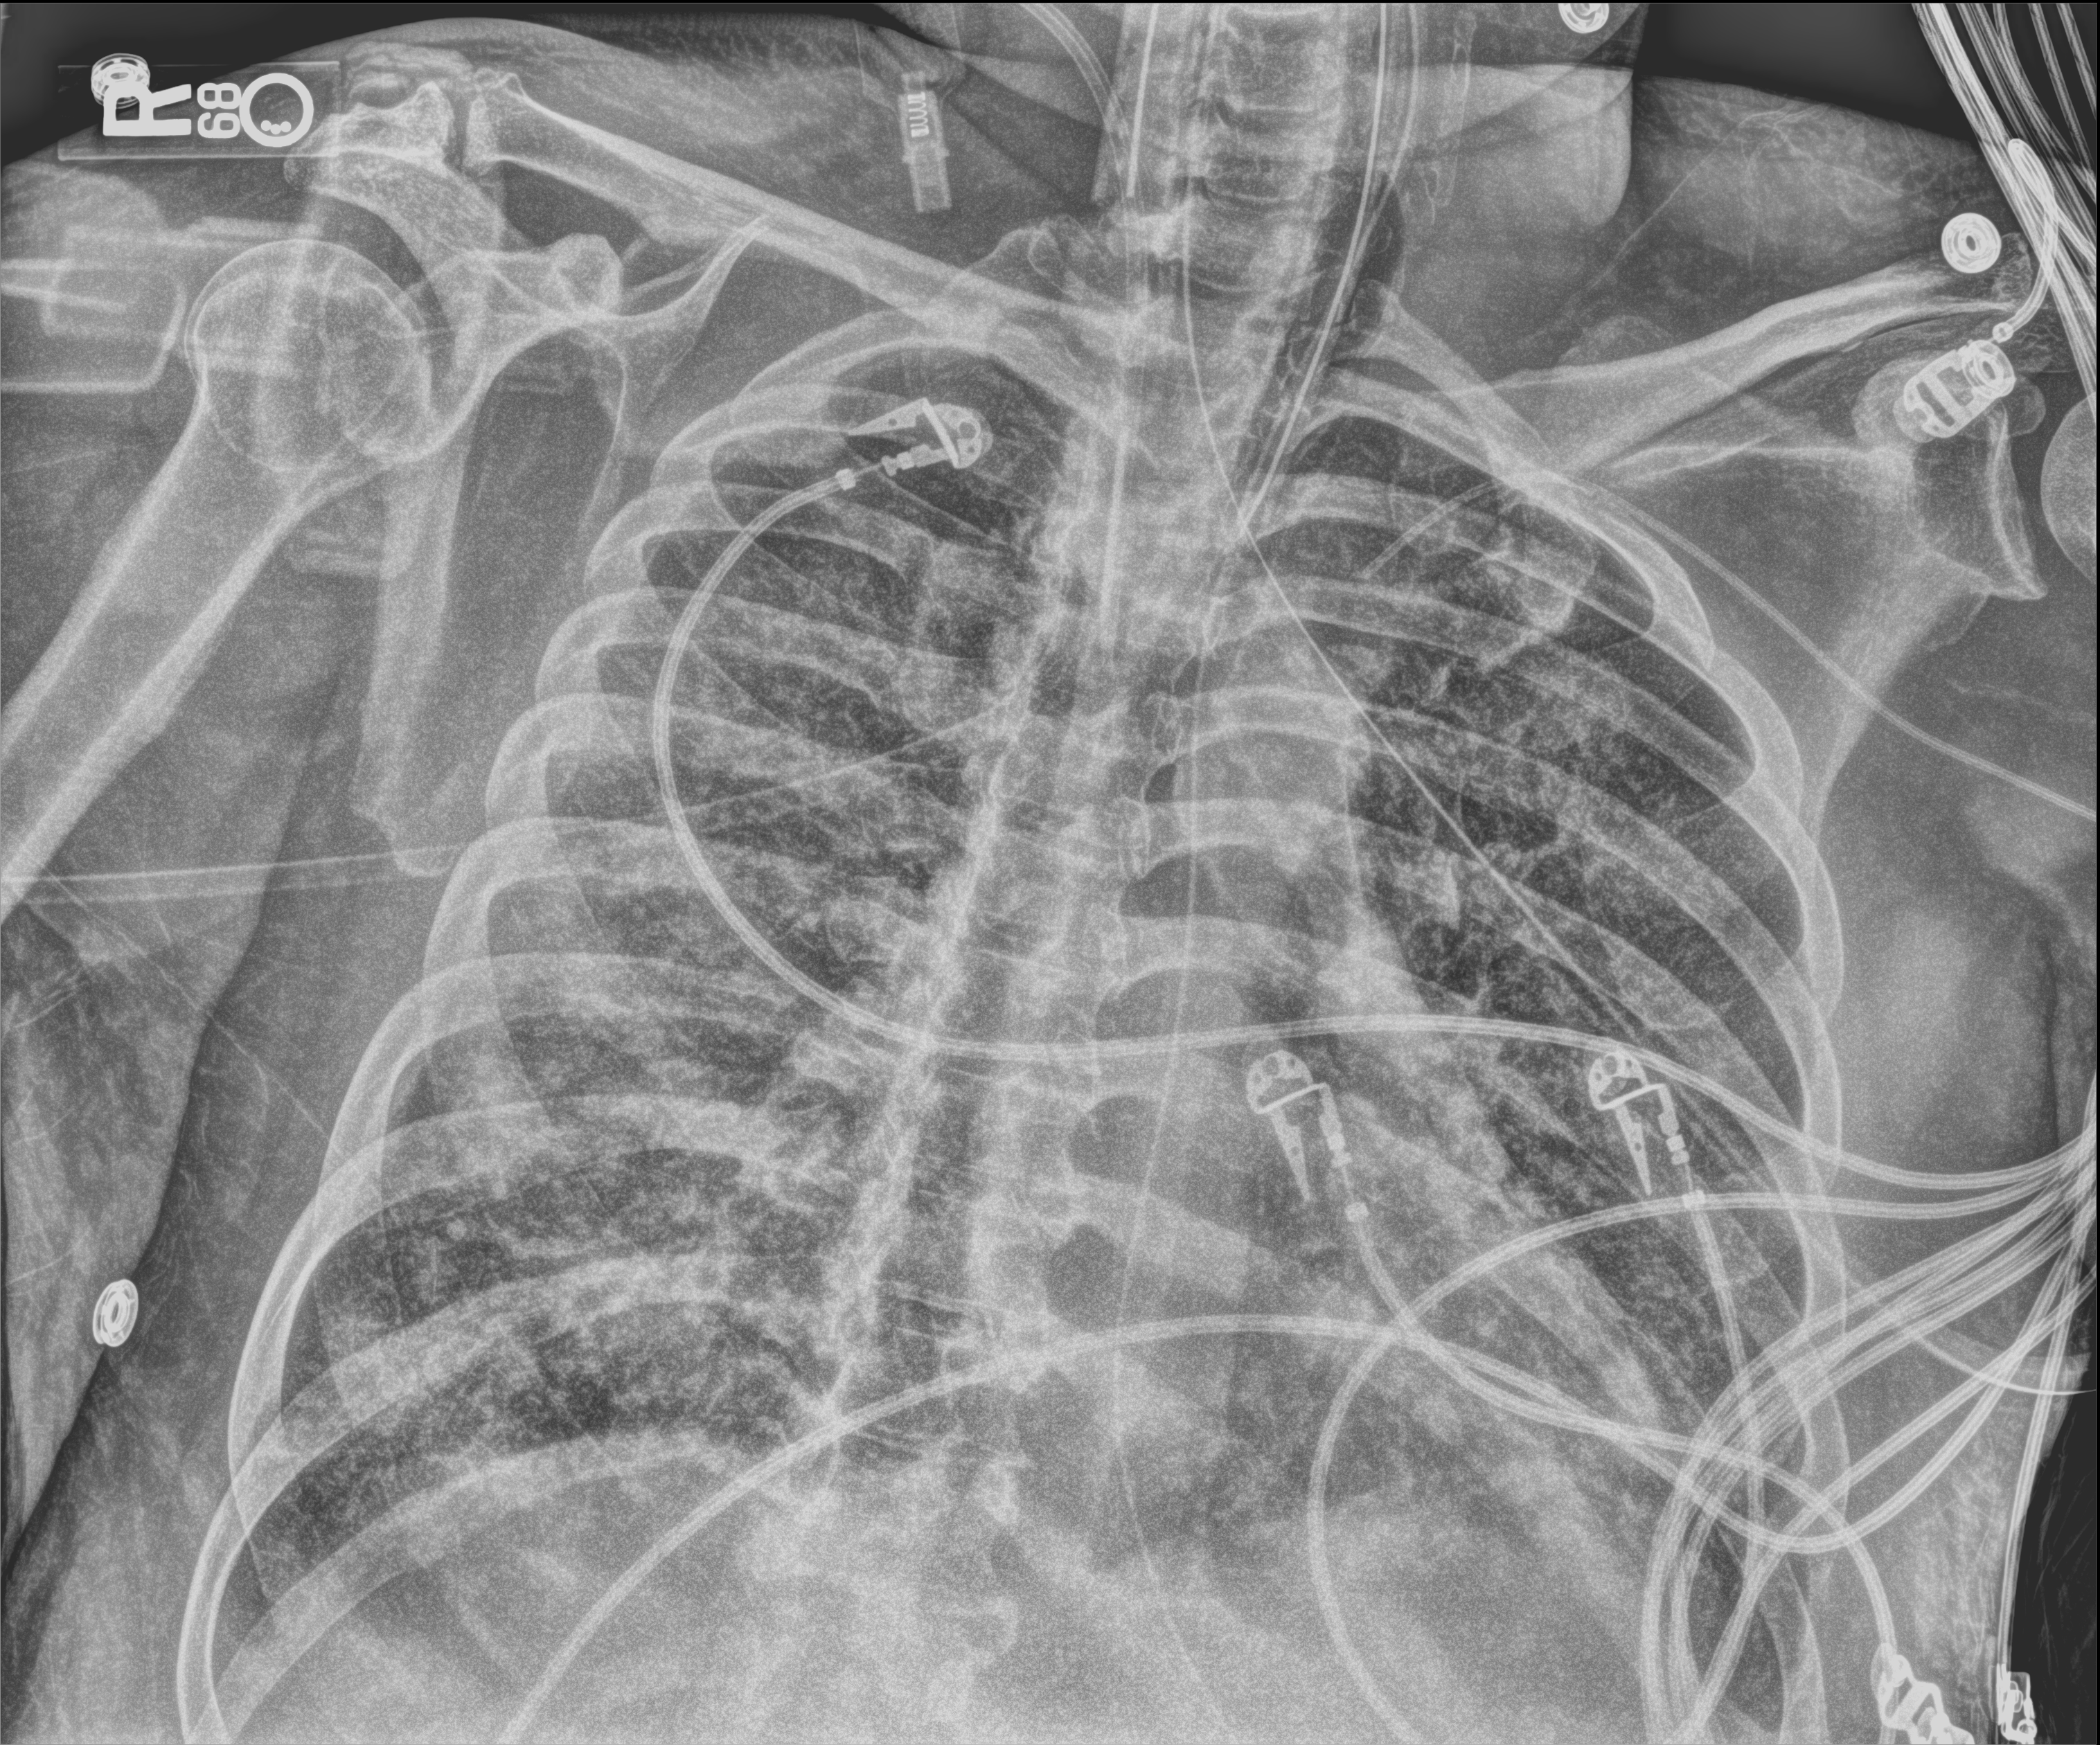
Portable chest radiograph, anteroposterior (AP) projection. Male patient hospitalised with COVID-19, age 60–74 years.
Hospital-stay facts (about this admission, not read from this image; timing relative to this image not recorded):
- admitted to intensive care during this hospital stay: yes
- mechanically ventilated during this hospital stay: yes